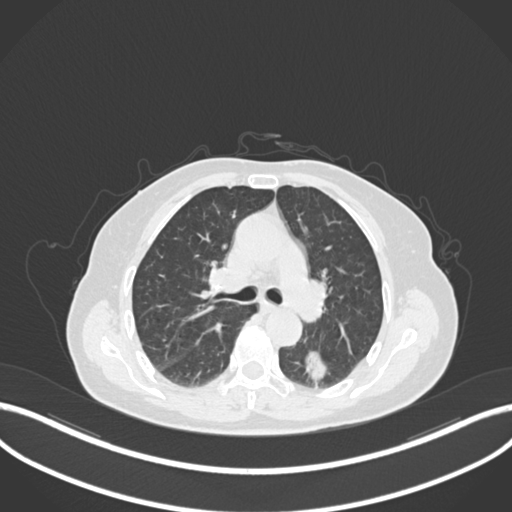
Chest CT, one axial slice; position 534 of 727 along the scan axis; reconstruction kernel B30f; 120 kVp; lung window (W 1500 / L -600 HU); 512 × 512 image matrix, field of view 400 × 400 mm. Patient: female, 70 years. From the clinical record (not read from this slice): clinical TNM (as recorded): T1c N0 M0.
Outlined on this slice (rectangle marked by the reading radiologist):
- lung tumour (recorded histology: adenocarcinoma): box from (x=301, y=349) to (x=332, y=385) px